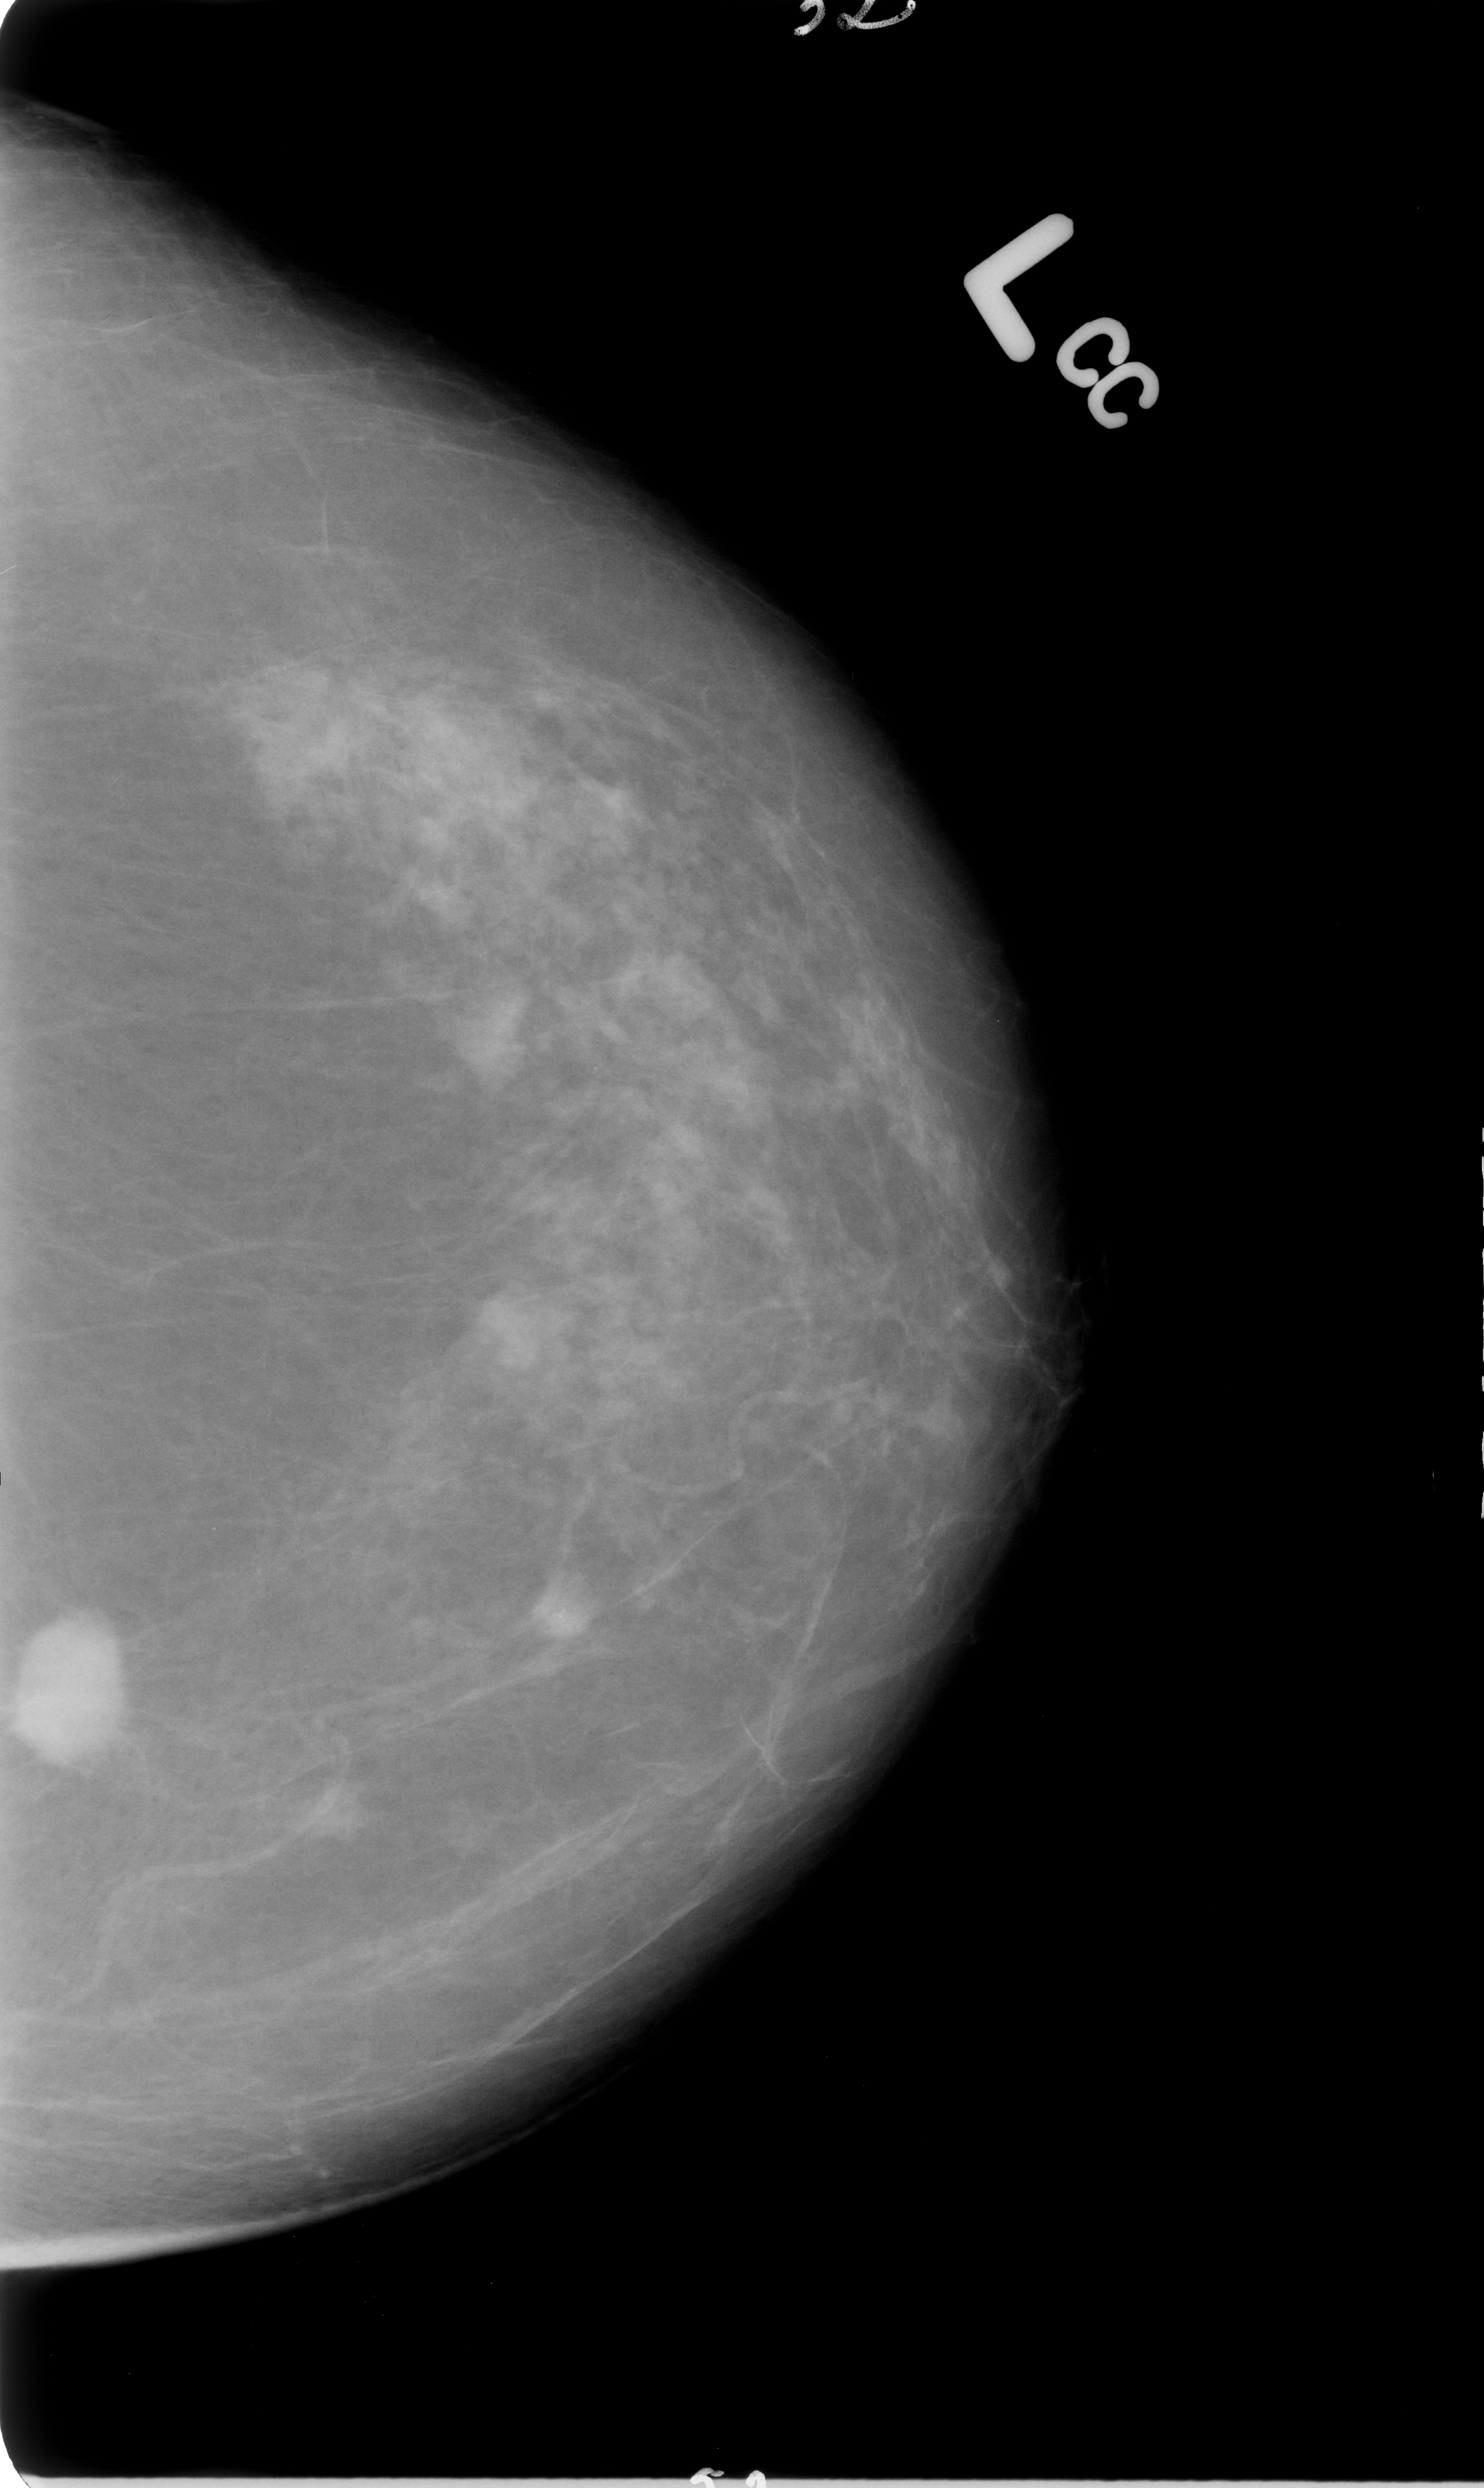
Scanned film-screen mammogram, left breast, CC view.
Marked findings (only marked abnormalities are described; nothing is implied about the rest of the image): mass, shape oval, margins spiculated; BI-RADS assessment category 4; subtlety rating 5 on a 1 (subtle) to 5 (obvious) scale; pathology (as recorded): malignant.